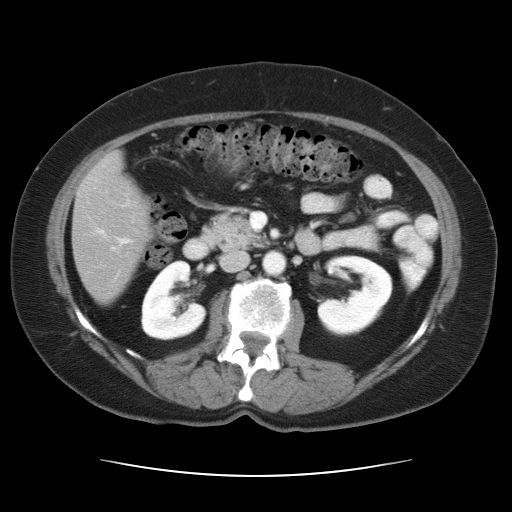
Contrast-enhanced abdominal CT, one axial slice; slice 12 of 34 in the series (ordered by position); reconstruction kernel STANDARD; intravenous contrast given; soft-tissue window (W 400 / L 40 HU); 512 × 512 image matrix, field of view 360 × 360 mm. Female patient, age 65 years. Case-level facts recorded for this patient, not image findings: diagnosis: colorectal cancer liver metastases, imaged before liver resection.
Annotated regions visible in this slice (outlined manually by an expert reader):
- hepatic veins: bounding box <99,231,103,233> (left, top, right, bottom; pixels)
- liver: <74,155,148,301>
- planned liver remnant (the part of the liver to remain after resection): <74,155,148,301>
- portal vein (with intrahepatic branches): <119,239,129,243>